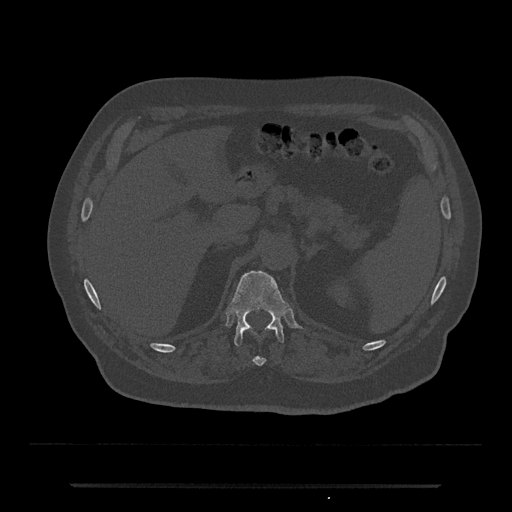
CT including the spine, one axial slice; slice 608 of 797 in the series (ordered by position); bone window (W 1800 / L 400 HU); 512 × 512 image matrix. Patient: male, 80 years. Case-level facts recorded for this patient, not image findings: primary cancer: prostate; vertebrae with lytic lesions (as recorded): L1, T11.
Outlined on this slice (semi-automatically segmented with operator editing):
- T11 vertebra: bounding box [x1, y1, x2, y2] px = [253, 357, 265, 366]
- T12 vertebra: [228, 270, 289, 346]